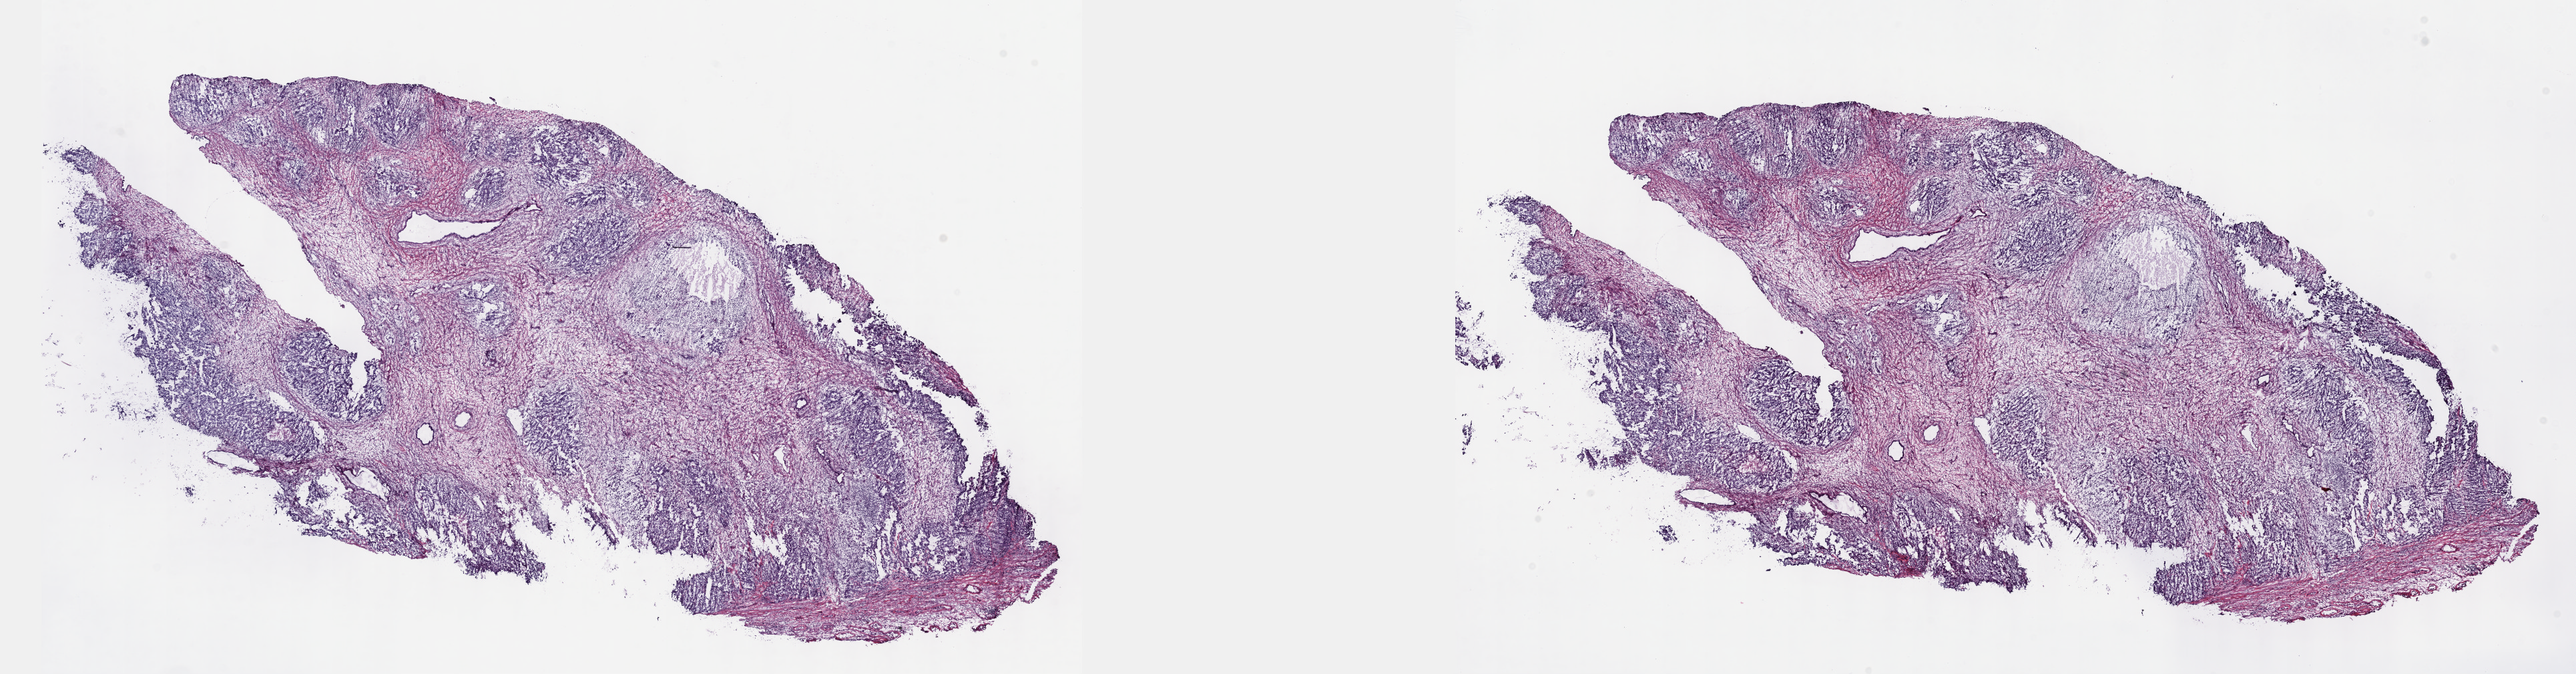
Whole-slide histology image, H&E, shown as a low-resolution overview of the whole scanned area (about 31.2 x 8.2 mm, acquisition: 40x scan). Patient sex: male. Slide review estimates, as recorded: tumour cells 90%, tumour nuclei 95%, normal cells 0%, stromal cells 10%, necrosis 0%. Inflammatory infiltration, as recorded: lymphocyte infiltration 0%, monocyte infiltration 0%, neutrophil infiltration 0%.
Specimen: frozen section from the top of the tissue portion; primary tumour sample from the testis.